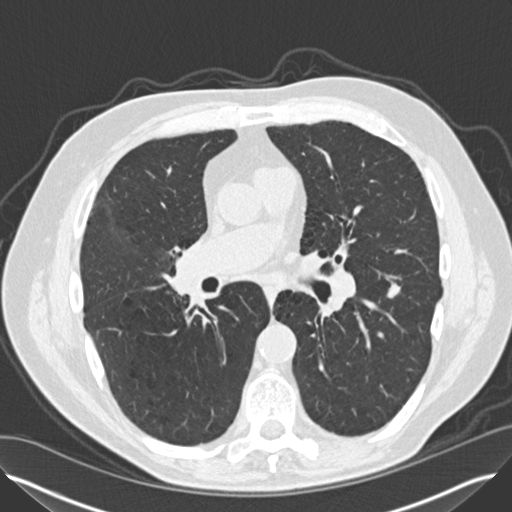
Low-dose screening chest CT, axial slice, second annual screen, lung window (W 1500 / L -600 HU), slice 74 of 149 in the series, 512 × 512 image matrix, field of view 370 × 370 mm. Male, age 65 years at enrolment. Current smoker at enrolment.
- Expert-annotated lung lesion, bounding box [x1, y1, x2, y2] px = [371, 275, 414, 312].
- Reader record for this screening exam (exam-level; its link to the box is not recorded): non-calcified nodule or mass ≥4 mm, left lower lobe, 12 × 8 mm, smooth margins, soft tissue attenuation, pre-existing on the prior screen: yes; interval growth: yes.
- Participant outcome: lung cancer diagnosed 67 days after this screen — non-small cell carcinoma, left lower lobe, right hilum, poorly differentiated (G3), stage IV (AJCC 6th edition), 5 mm at pathology.